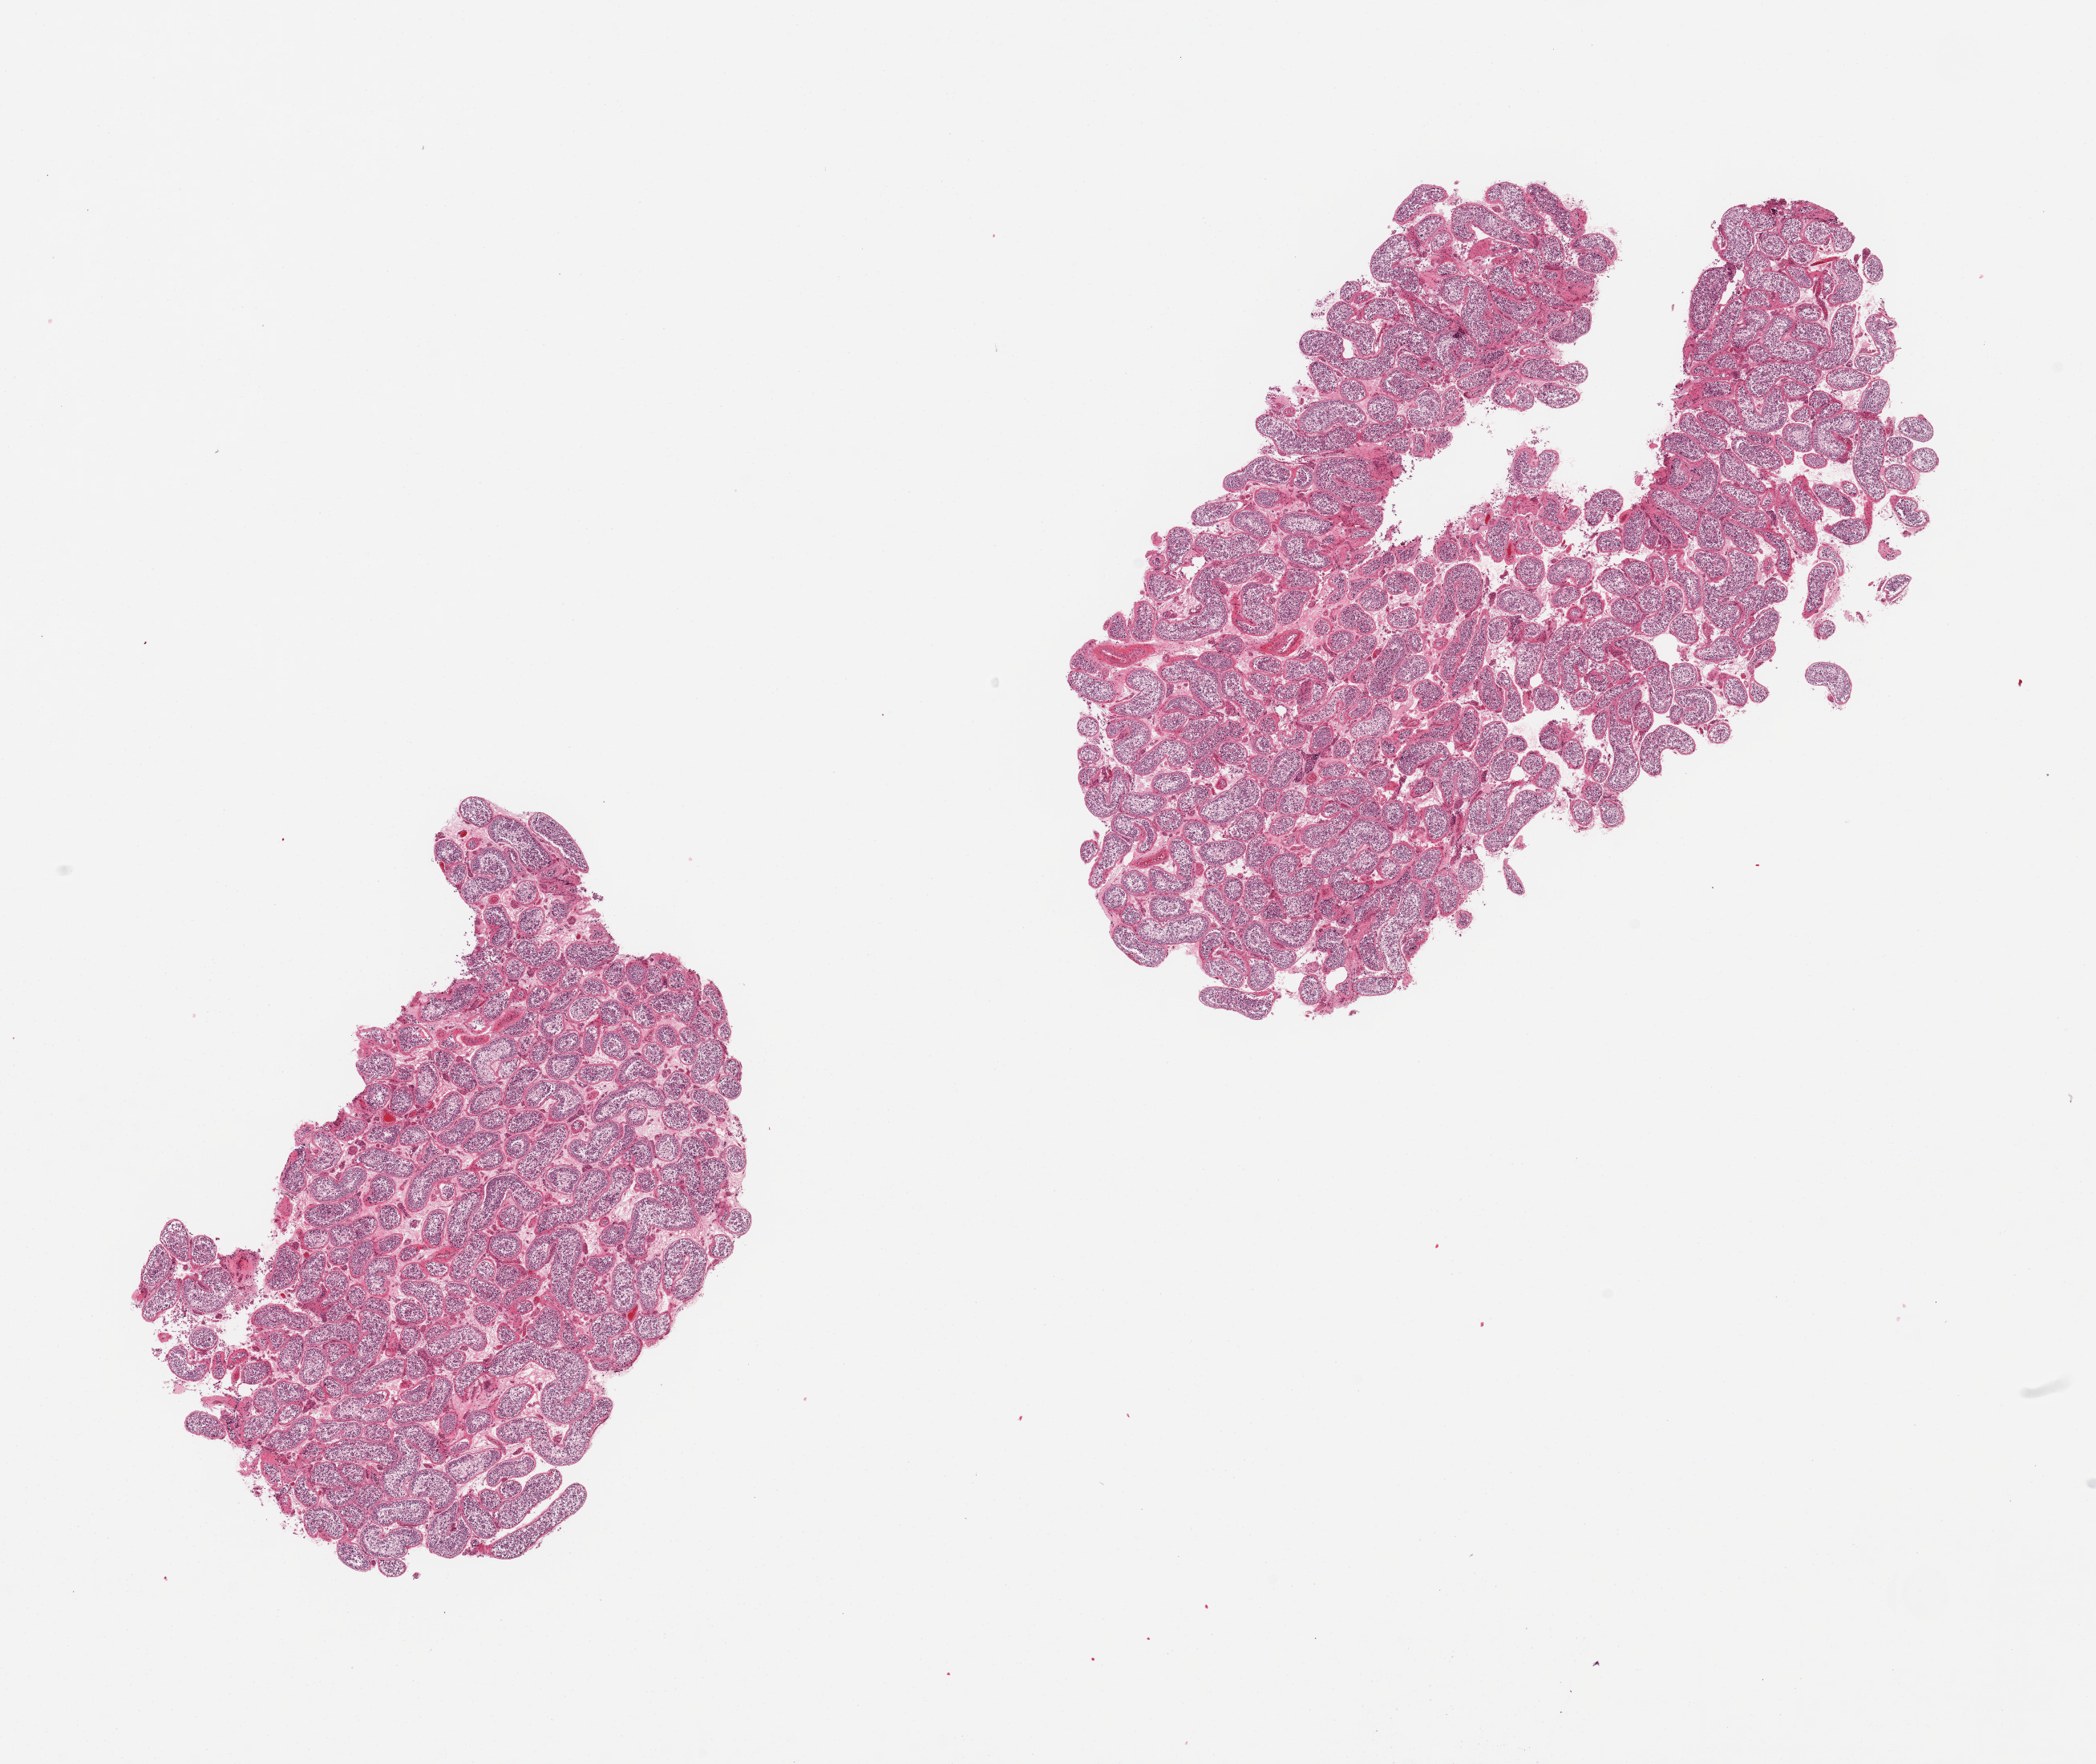
Whole-slide image, hematoxylin and eosin (H&E) stain — a low-resolution overview of the entire scanned area, about 20.7 x 17.4 mm (from a 20x scan). PAXgene-fixed, paraffin-embedded tissue. Target tissue: testis. Donor tissue sample. Donor sex: male.
Reviewer comment on this tissue sample: 2 pieces; active spermatogenesis.